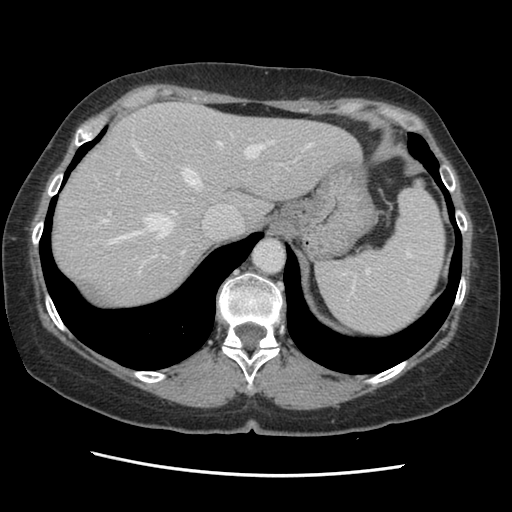
Contrast-enhanced abdominal CT, one axial slice. Slice 107 of 141 in the series (ordered by position). Soft-tissue window (W 400 / L 40 HU). 2.5 mm slice thickness. 512 × 512 image matrix, field of view 330 × 330 mm. Female patient, age 61 years. From the clinical record (not read from this slice): diagnosis: colorectal cancer liver metastases, imaged before liver resection; multiple liver metastases: no; largest metastasis: 2.4 cm; chemotherapy before resection: no.
Outlined on this slice (outlined manually by an expert reader):
- hepatic veins: bounding box (x1, y1, x2, y2) in pixels: (94, 133, 313, 276)
- liver: (53, 103, 359, 310)
- planned liver remnant (the part of the liver to remain after resection): (53, 103, 359, 310)
- portal vein (with intrahepatic branches): (108, 170, 166, 273)